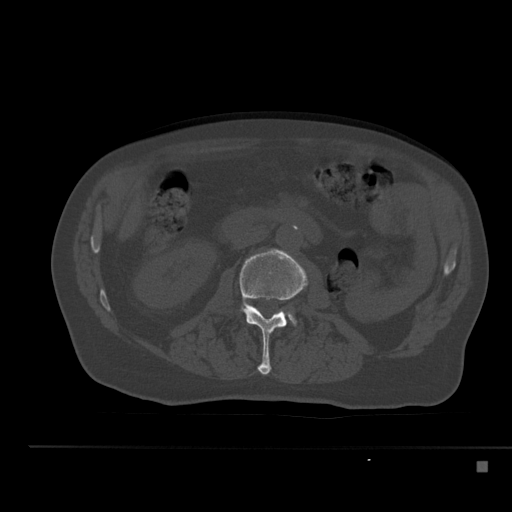
CT including the spine, one axial slice. Position 182 of 517 along the scan axis. Reconstruction kernel Br40s. 120 kVp. Bone window (W 1800 / L 400 HU). 512 × 512 image matrix, field of view 408 × 408 mm. Patient: male, 70 years. From the clinical record (not read from this slice): primary cancer: renal; vertebrae with lytic lesions (as recorded): T4, T6, T10, T12, L3, L4, L5.
Annotated regions visible in this slice (semi-automatically segmented with operator editing):
- L2 vertebra: box from (x=239, y=249) to (x=307, y=375) px
- L3 vertebra: (x=290, y=316)–(x=296, y=324)